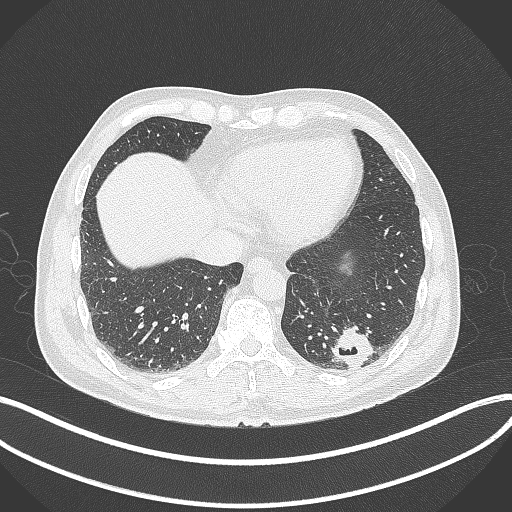
Chest CT, one axial slice. Reconstruction kernel B70f. 120 kVp. Lung window (W 1500 / L -600 HU). 1 mm slice thickness. 512 × 512 image matrix, field of view 400 × 400 mm. Patient: male, 54 years. Case-level facts recorded for this patient, not image findings: clinical TNM (as recorded): T1c N0 M1.
Structures marked on this image (bounding box drawn by a radiologist):
- lung tumour (recorded histology: adenocarcinoma): bounding box [x1, y1, x2, y2] px = [330, 323, 377, 370]